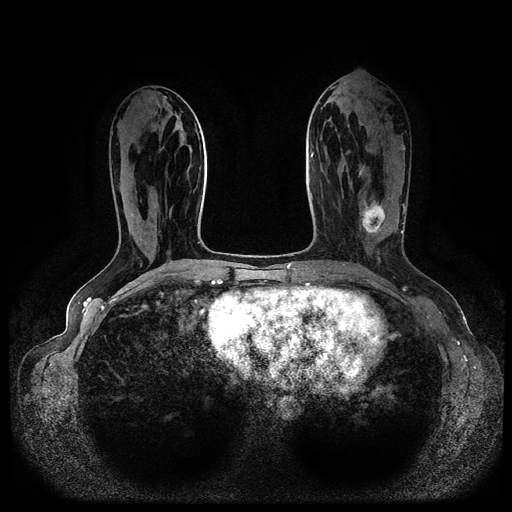
Breast MRI (dynamic contrast-enhanced, multi-phase), one axial slice. Slice 41 of 116 in the series (ordered by position). Dynamic contrast-enhanced series, time point 2 of 5 at this slice position (early post-contrast). 1.5 T. TE 2.6 ms, TR 5.3 ms. 2 mm slice thickness. 512 × 512 image matrix, field of view 350 × 350 mm. Patient: female, 45 years.
Structures marked on this image (semi-automatically segmented with operator editing):
- breast lesion (labelled 'tumour' in the annotation; benign lesions carry a separate 'benign' label): bounding box (x1, y1, x2, y2) in pixels: (359, 200, 390, 239)